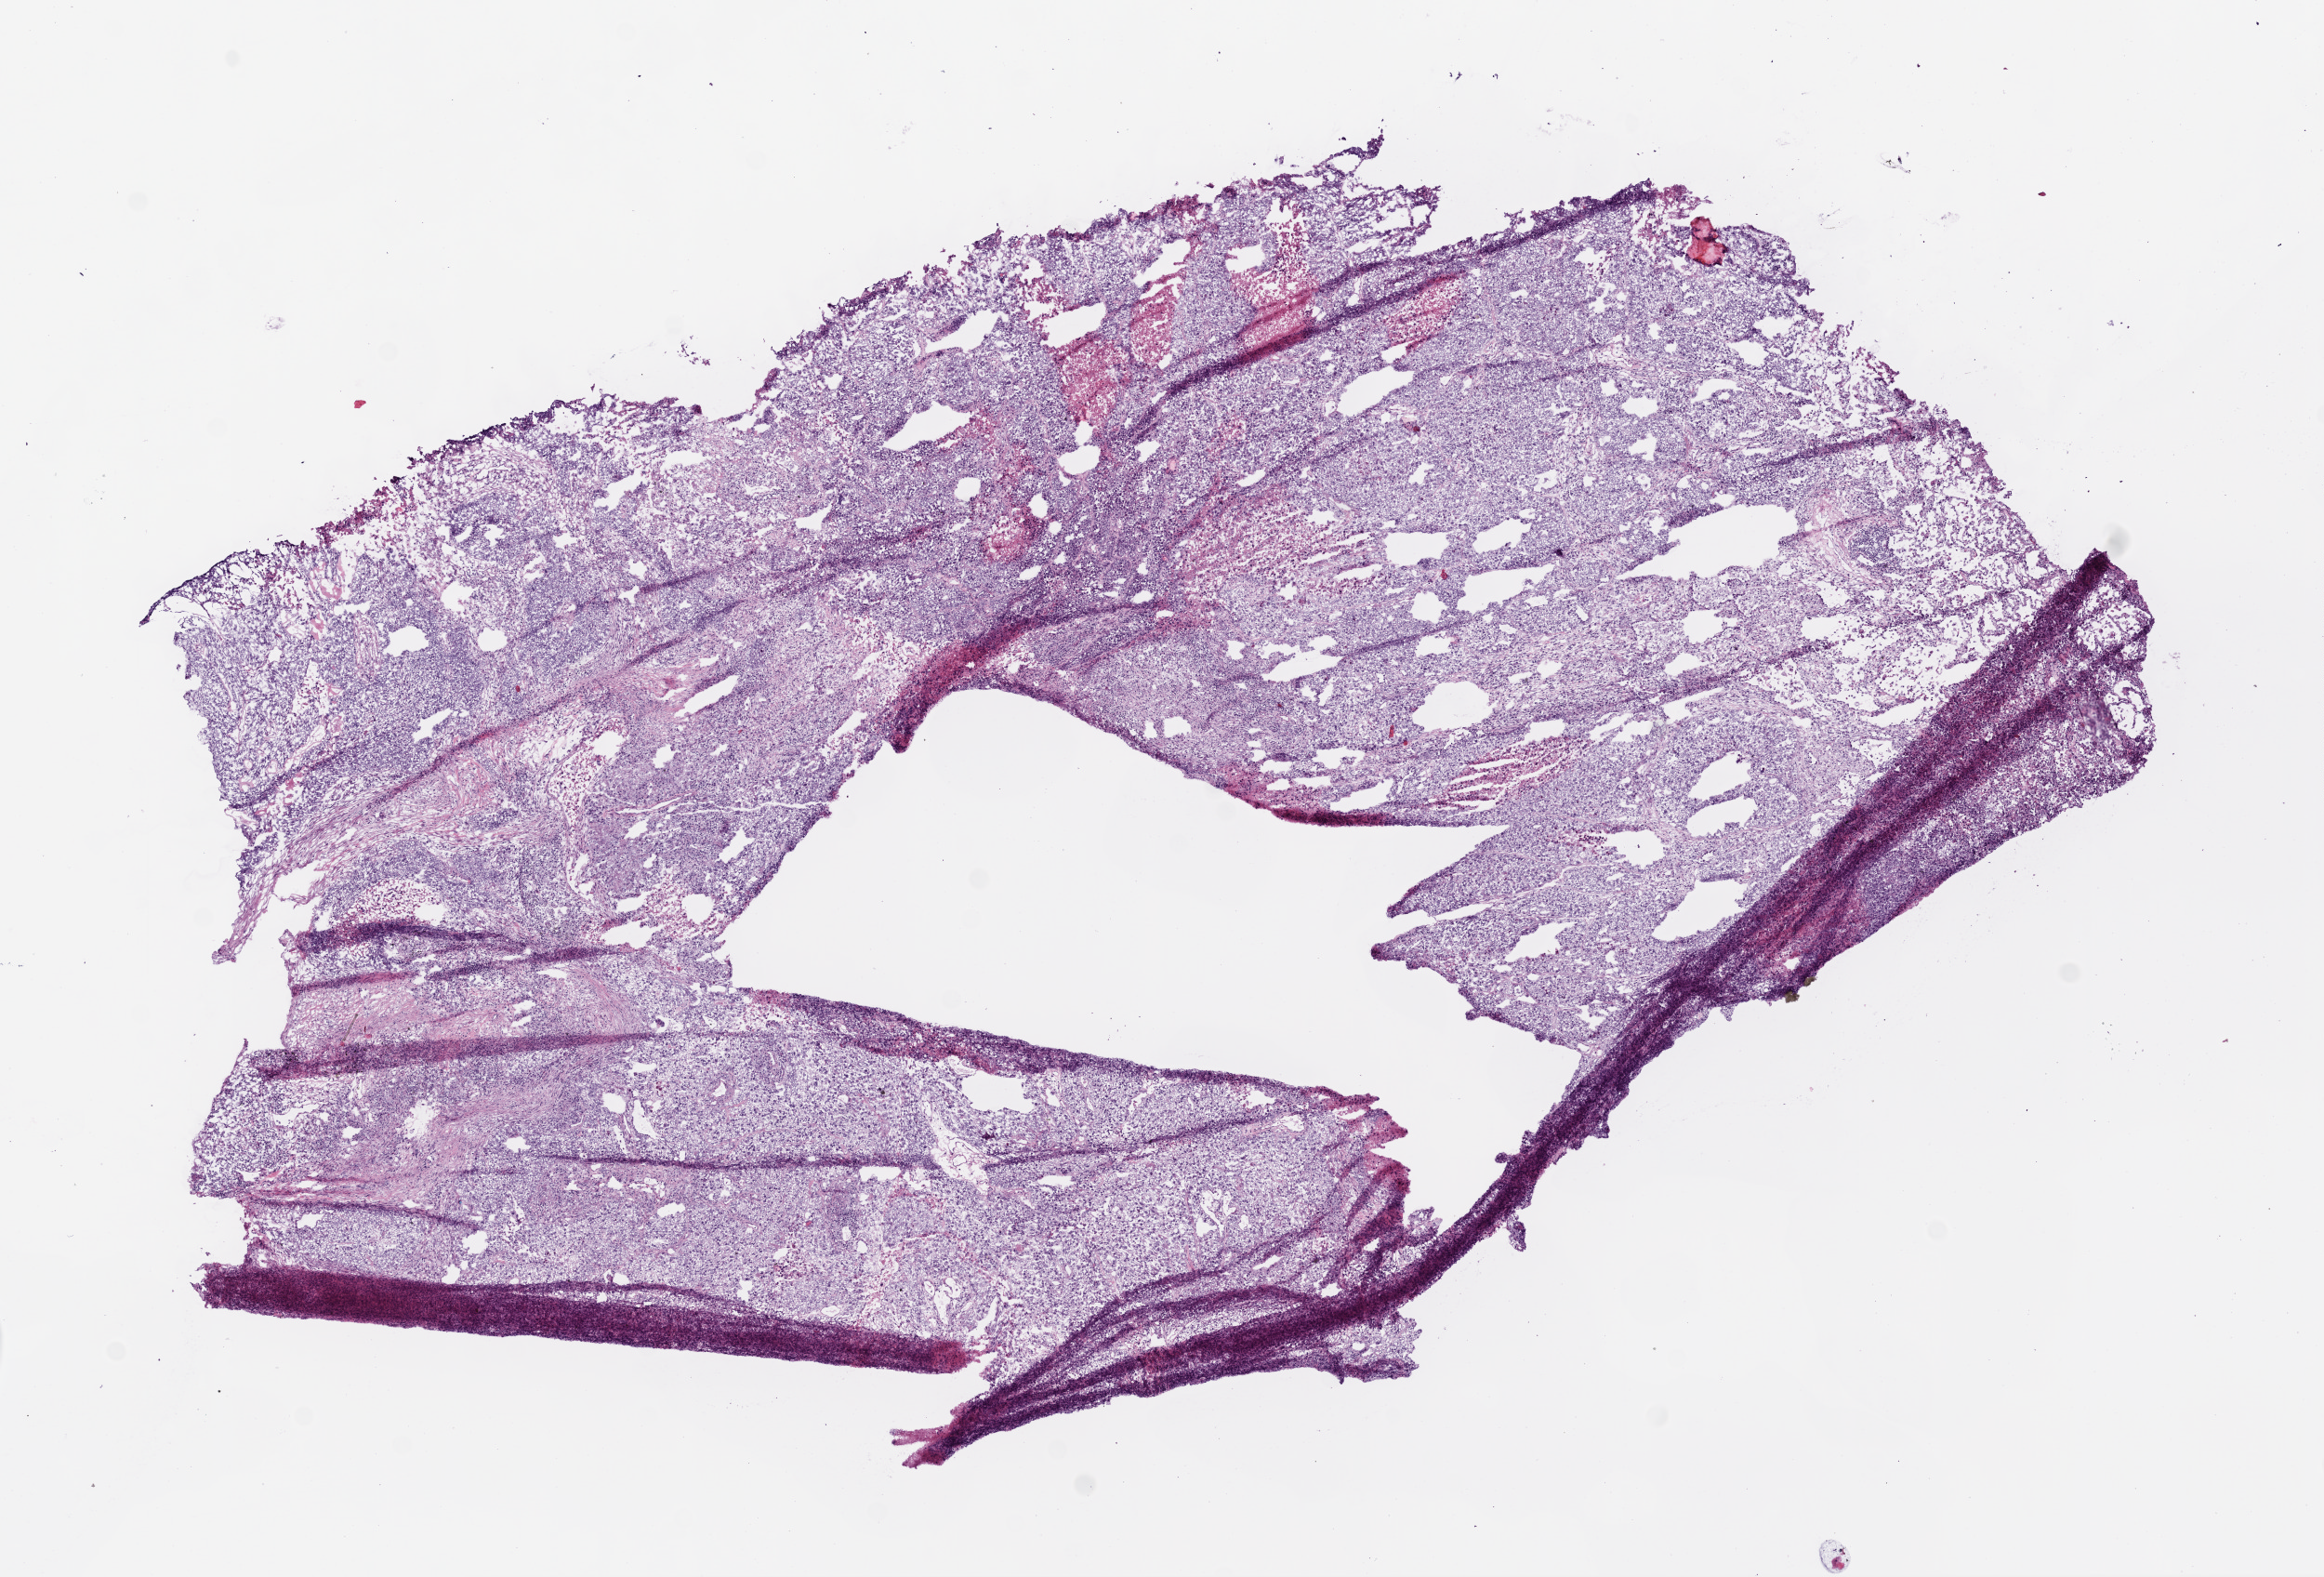
Whole-slide histology image, H&E-stained — low-resolution overview of the scanned area, about 10.0 x 6.8 mm (acquisition: 20x scan). Frozen section. Primary tumour sample from the lung. Female, age 83 years at initial diagnosis. Slide review estimates, as recorded: tumour cells 83%, tumour nuclei 85%, normal cells 7%, stromal cells 5%, necrosis 5%.
AJCC pathologic stage: IB. Diagnosis: Squamous cell carcinoma, NOS. TNM: T1 N0 M0.